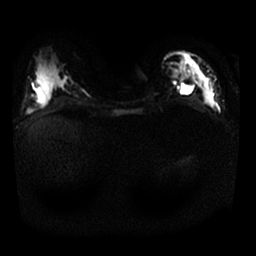
Breast MRI, one axial slice; slice 13 of 25 in the series (ordered by position); diffusion-weighted series; image 2 of 4 stored at this slice position (different b-values; order by instance number); 1.5 T; 256 × 256 image matrix. Female patient.
Outlined on this slice (expert manual segmentation):
- tumour on diffusion-weighted imaging: bounding box (x1, y1, x2, y2) in pixels: (192, 64, 215, 107)